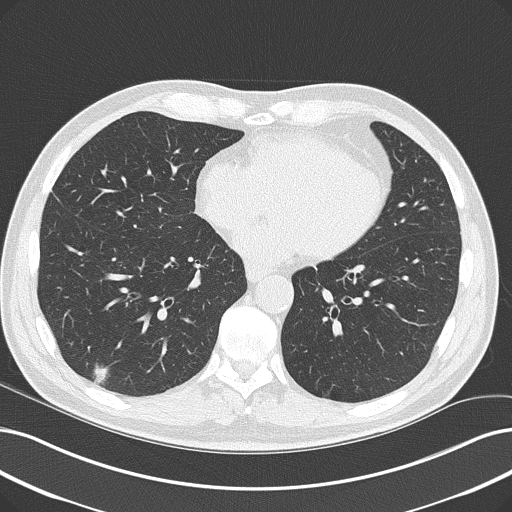
Low-dose screening chest CT, one axial slice. Slice 90 of 228 in the series (ordered by position). Lung window (W 1500 / L -600 HU). 2 mm slice thickness. 512 × 512 image matrix, field of view 366 × 366 mm.
Structures marked on this image (outlined manually by an expert reader):
- lesion 1 (tumor, lower lobe of right lung): bounding box [x1, y1, x2, y2] px = [93, 363, 108, 384]